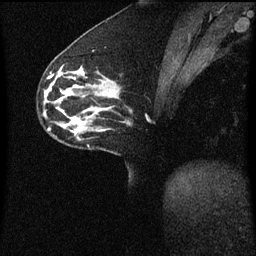
Breast MRI (dynamic contrast-enhanced), one sagittal slice. Position 22 of 60 along the scan axis. Dynamic contrast-enhanced series, image 2 of 3 at this slice position (ordered by acquisition). 1.5 T. TE 4.2 ms, TR 8.4 ms. 256 × 256 image matrix, field of view 200 × 200 mm. Patient: female, 33 years. Case-level facts recorded for this patient, not image findings: setting: breast cancer imaged before/during neoadjuvant chemotherapy; receptor status: triple-negative.
Outlined on this slice (semi-automatically segmented with operator editing):
- analysis volume of interest (the breast-tissue region the enhancement analysis was run in; not a lesion): bounding box (x1, y1, x2, y2) in pixels: (76, 66, 120, 113)
- tumour enhancement mask (voxels above the 70 % enhancement threshold inside the analysis volume of interest): (102, 84, 111, 97)